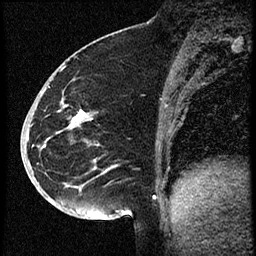
Breast MRI (dynamic contrast-enhanced), one sagittal slice; position 25 of 60 along the scan axis; dynamic contrast-enhanced study with each time point stored as its own series, time point 2 of 3 at this slice position (early post-contrast, ordered by acquisition time); 1.5 T; TE 4.2 ms, TR 18.9 ms; 256 × 256 image matrix, field of view 200 × 200 mm. Female patient. From the clinical record (not read from this slice): setting: breast cancer imaged before/during neoadjuvant chemotherapy; receptor status: HR-positive, HER2-negative.
Annotated regions visible in this slice (semi-automatically segmented with operator editing):
- analysis volume of interest (the breast-tissue region the enhancement analysis was run in; not a lesion): bounding box (x1, y1, x2, y2) in pixels: (30, 87, 114, 173)
- tumour enhancement mask (voxels above the 100 % enhancement threshold inside the analysis volume of interest): (74, 112, 86, 122)